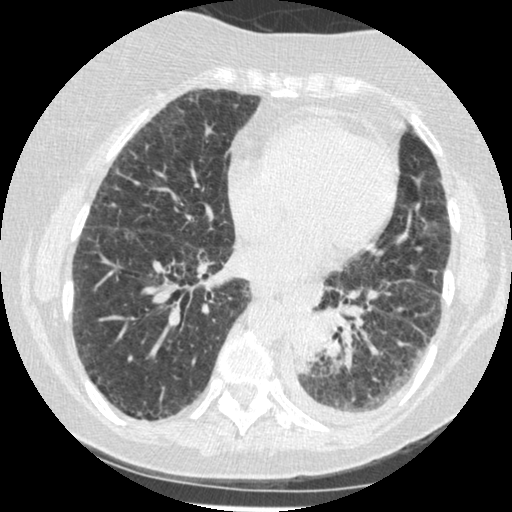
Low-dose screening chest CT, one axial slice; slice 86 of 341 in the series (ordered by position); reconstruction kernel STANDARD; lung window (W 1500 / L -600 HU); 1.25 mm slice thickness; 512 × 512 image matrix, field of view 310 × 310 mm.
Annotated regions visible in this slice (expert manual segmentation):
- lesion 1 (tumor, lower lobe of left lung): bounding box (x1, y1, x2, y2) in pixels: (291, 318, 323, 373)